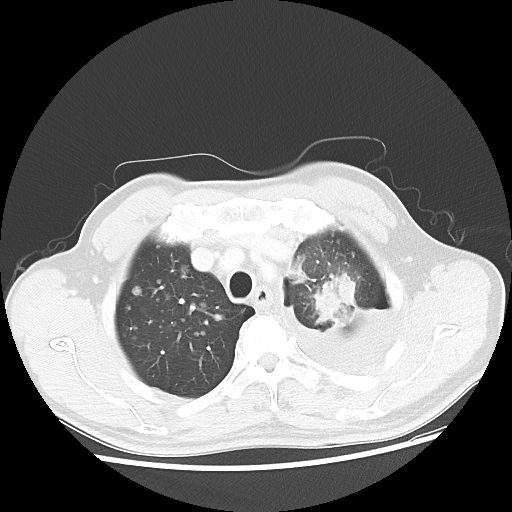
Chest CT, one axial slice; slice 39 of 47 in the series (ordered by position); reconstruction kernel LUNG; 100 kVp; lung window (W 1500 / L -600 HU); 5 mm slice thickness; 512 × 512 image matrix, field of view 362 × 362 mm. Patient: male, 55 years. Case-level facts recorded for this patient, not image findings: clinical TNM (as recorded): T2 N3 M1a; histopathological grade: G3.
Annotated regions visible in this slice (bounding box drawn by a radiologist):
- lung tumour (recorded histology: squamous cell carcinoma): bounding box [x1, y1, x2, y2] px = [310, 270, 357, 330]